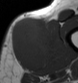
MRI of an extremity soft-tissue mass, one axial slice. Slice 15 of 43 in the series (ordered by position). MR volume resampled by the dataset authors to the PET/CT grid (not the native acquisition matrix). 78 × 83 image matrix, field of view 76 × 81 mm. Male patient. Case-level facts recorded for this patient, not image findings: histological type: pleiomorphic leiomyosarcoma; grade: high; site of the primary tumour: left thigh.
Structures marked on this image (expert contour drawn on MRI and transferred to this co-registered scan by the dataset authors):
- gross tumour volume including surrounding oedema: bounding box [x1, y1, x2, y2] px = [9, 17, 60, 68]
- gross tumour volume (mass): [9, 17, 55, 68]